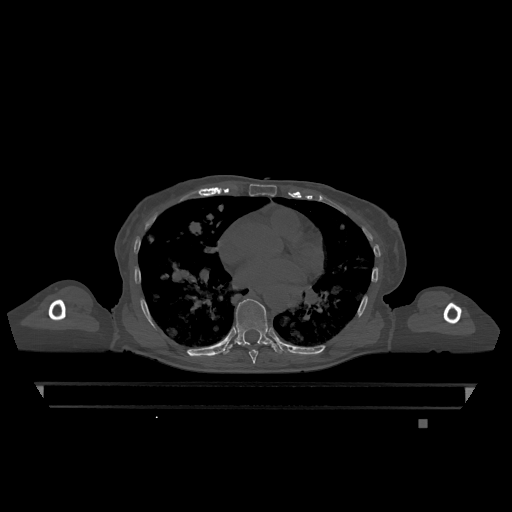
CT including the spine, one axial slice. Slice 708 of 1317 in the series (ordered by position). Bone window (W 1800 / L 400 HU). 512 × 512 image matrix, field of view 500 × 500 mm. Female patient, age 74 years. Case-level facts recorded for this patient, not image findings: primary cancer: lung.
Outlined on this slice (semi-automatic segmentation, software-assisted and operator-edited):
- T7 vertebra: bounding box <249,350,258,364> (left, top, right, bottom; pixels)
- T9 vertebra: <222,299,282,355>